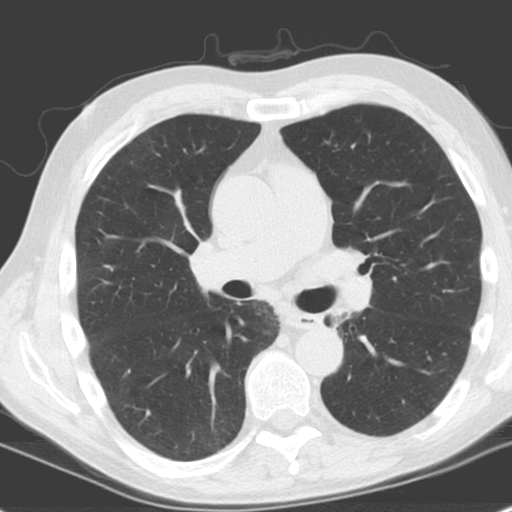
Chest CT (low-dose screening protocol), one axial image; baseline screening round; lung window (W 1500 / L -600 HU); 3.2 mm slice thickness; standard (soft-tissue) reconstruction kernel (C); slice 79 of 185 in the series; 512 × 512 image matrix. Male participant, aged 61 years at enrolment. Former smoker at enrolment.
Expert reader's lesion annotation, bounding box <311,305,358,342> (left, top, right, bottom; pixels). No non-calcified nodule or mass ≥4 mm was recorded by the screening reader at this exam. Official screen result: negative screen, minor abnormalities not suspicious for lung cancer. Lung cancer was diagnosed 1146 days after this screen: squamous cell carcinoma, NOS, left upper lobe, left lower lobe, well differentiated (G1), stage IIB (AJCC 6th edition), 100 mm at pathology.